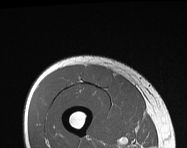
MRI of an extremity soft-tissue mass, one axial slice. Slice 43 of 114 in the series (ordered by position). MR volume resampled by the dataset authors to the PET/CT grid (not the native acquisition matrix). 3.27 mm slice thickness. 187 × 148 image matrix, field of view 183 × 145 mm. Male patient. From the clinical record (not read from this slice): histological type: pleiomorphic leiomyosarcoma; grade: intermediate; site of the primary tumour: right thigh.
Annotated regions visible in this slice (expert contour drawn on MRI and transferred to this co-registered scan by the dataset authors):
- gross tumour volume including surrounding oedema: bounding box <82,65,113,87> (left, top, right, bottom; pixels)